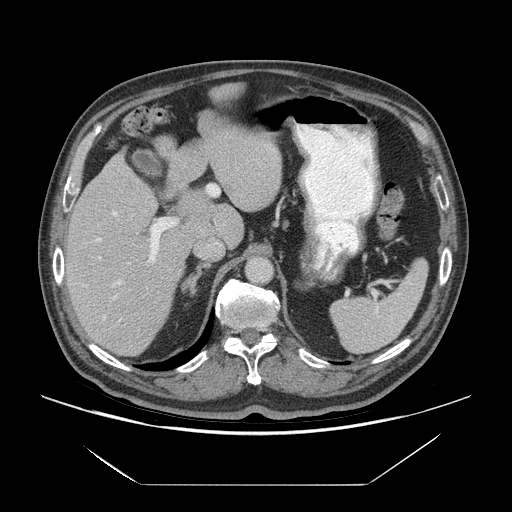
Contrast-enhanced abdominal CT (liver protocol), one axial slice; slice 42 of 75 in the series (ordered by position); reconstruction kernel STANDARD; soft-tissue window (W 400 / L 40 HU); 2.5 mm slice thickness; 512 × 512 image matrix, field of view 420 × 420 mm. Case-level facts recorded for this patient, not image findings: diagnosis: hepatocellular carcinoma (patient treated with transarterial chemoembolisation; whether this scan precedes or follows treatment is not stated here); TNM stage (as recorded): Stage-I; Child-Pugh class: A; tumour size: 5.8 cm.
Annotated regions visible in this slice (semi-automatic segmentation, software-assisted and operator-edited):
- liver parenchyma outside the tumour (the mass and vessels are separate outlines, so this box may not span the whole liver): bounding box [x1, y1, x2, y2] px = [66, 154, 242, 356]
- liver vessels: [84, 211, 178, 321]